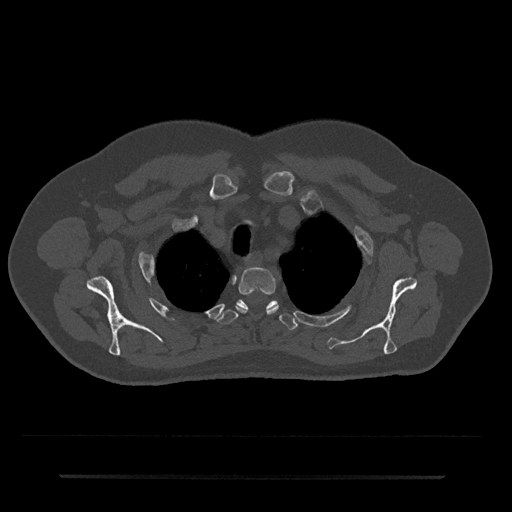
CT including the spine, one axial slice. Slice 589 of 797 in the series (ordered by position). Reconstruction kernel Br40s/3. 120 kVp. Bone window (W 1800 / L 400 HU). 512 × 512 image matrix, field of view 437 × 437 mm. Patient: male, 69 years. Case-level facts recorded for this patient, not image findings: primary cancer: prostate.
Structures marked on this image (semi-automatically segmented with operator editing):
- T2 vertebra: bounding box [x1, y1, x2, y2] px = [236, 268, 278, 314]
- T3 vertebra: [217, 299, 297, 330]